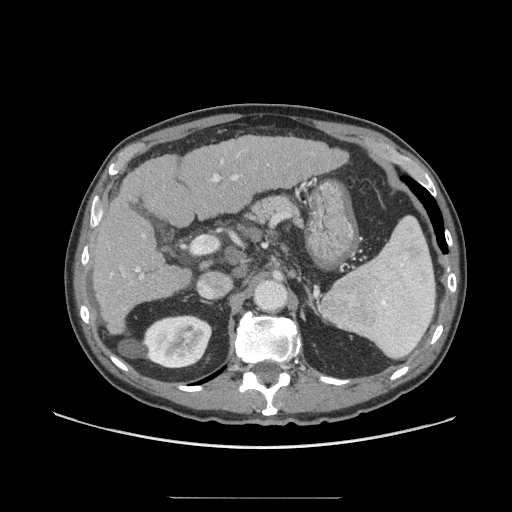
Contrast-enhanced abdominal CT (liver protocol), one axial slice; slice 38 of 71 in the series (ordered by position); reconstruction kernel STANDARD; 140 kVp; soft-tissue window (W 400 / L 40 HU); 2.5 mm slice thickness; 512 × 512 image matrix. From the clinical record (not read from this slice): diagnosis: hepatocellular carcinoma (patient treated with transarterial chemoembolisation; whether this scan precedes or follows treatment is not stated here); TNM stage (as recorded): Stage-I; Child-Pugh class: A; tumour differentiation: well differentiated; tumour nodularity: uninodular.
Outlined on this slice (semi-automatically segmented with operator editing):
- liver parenchyma outside the tumour (the mass and vessels are separate outlines, so this box may not span the whole liver): bounding box <90,136,346,334> (left, top, right, bottom; pixels)
- liver vessels: <110,154,240,279>